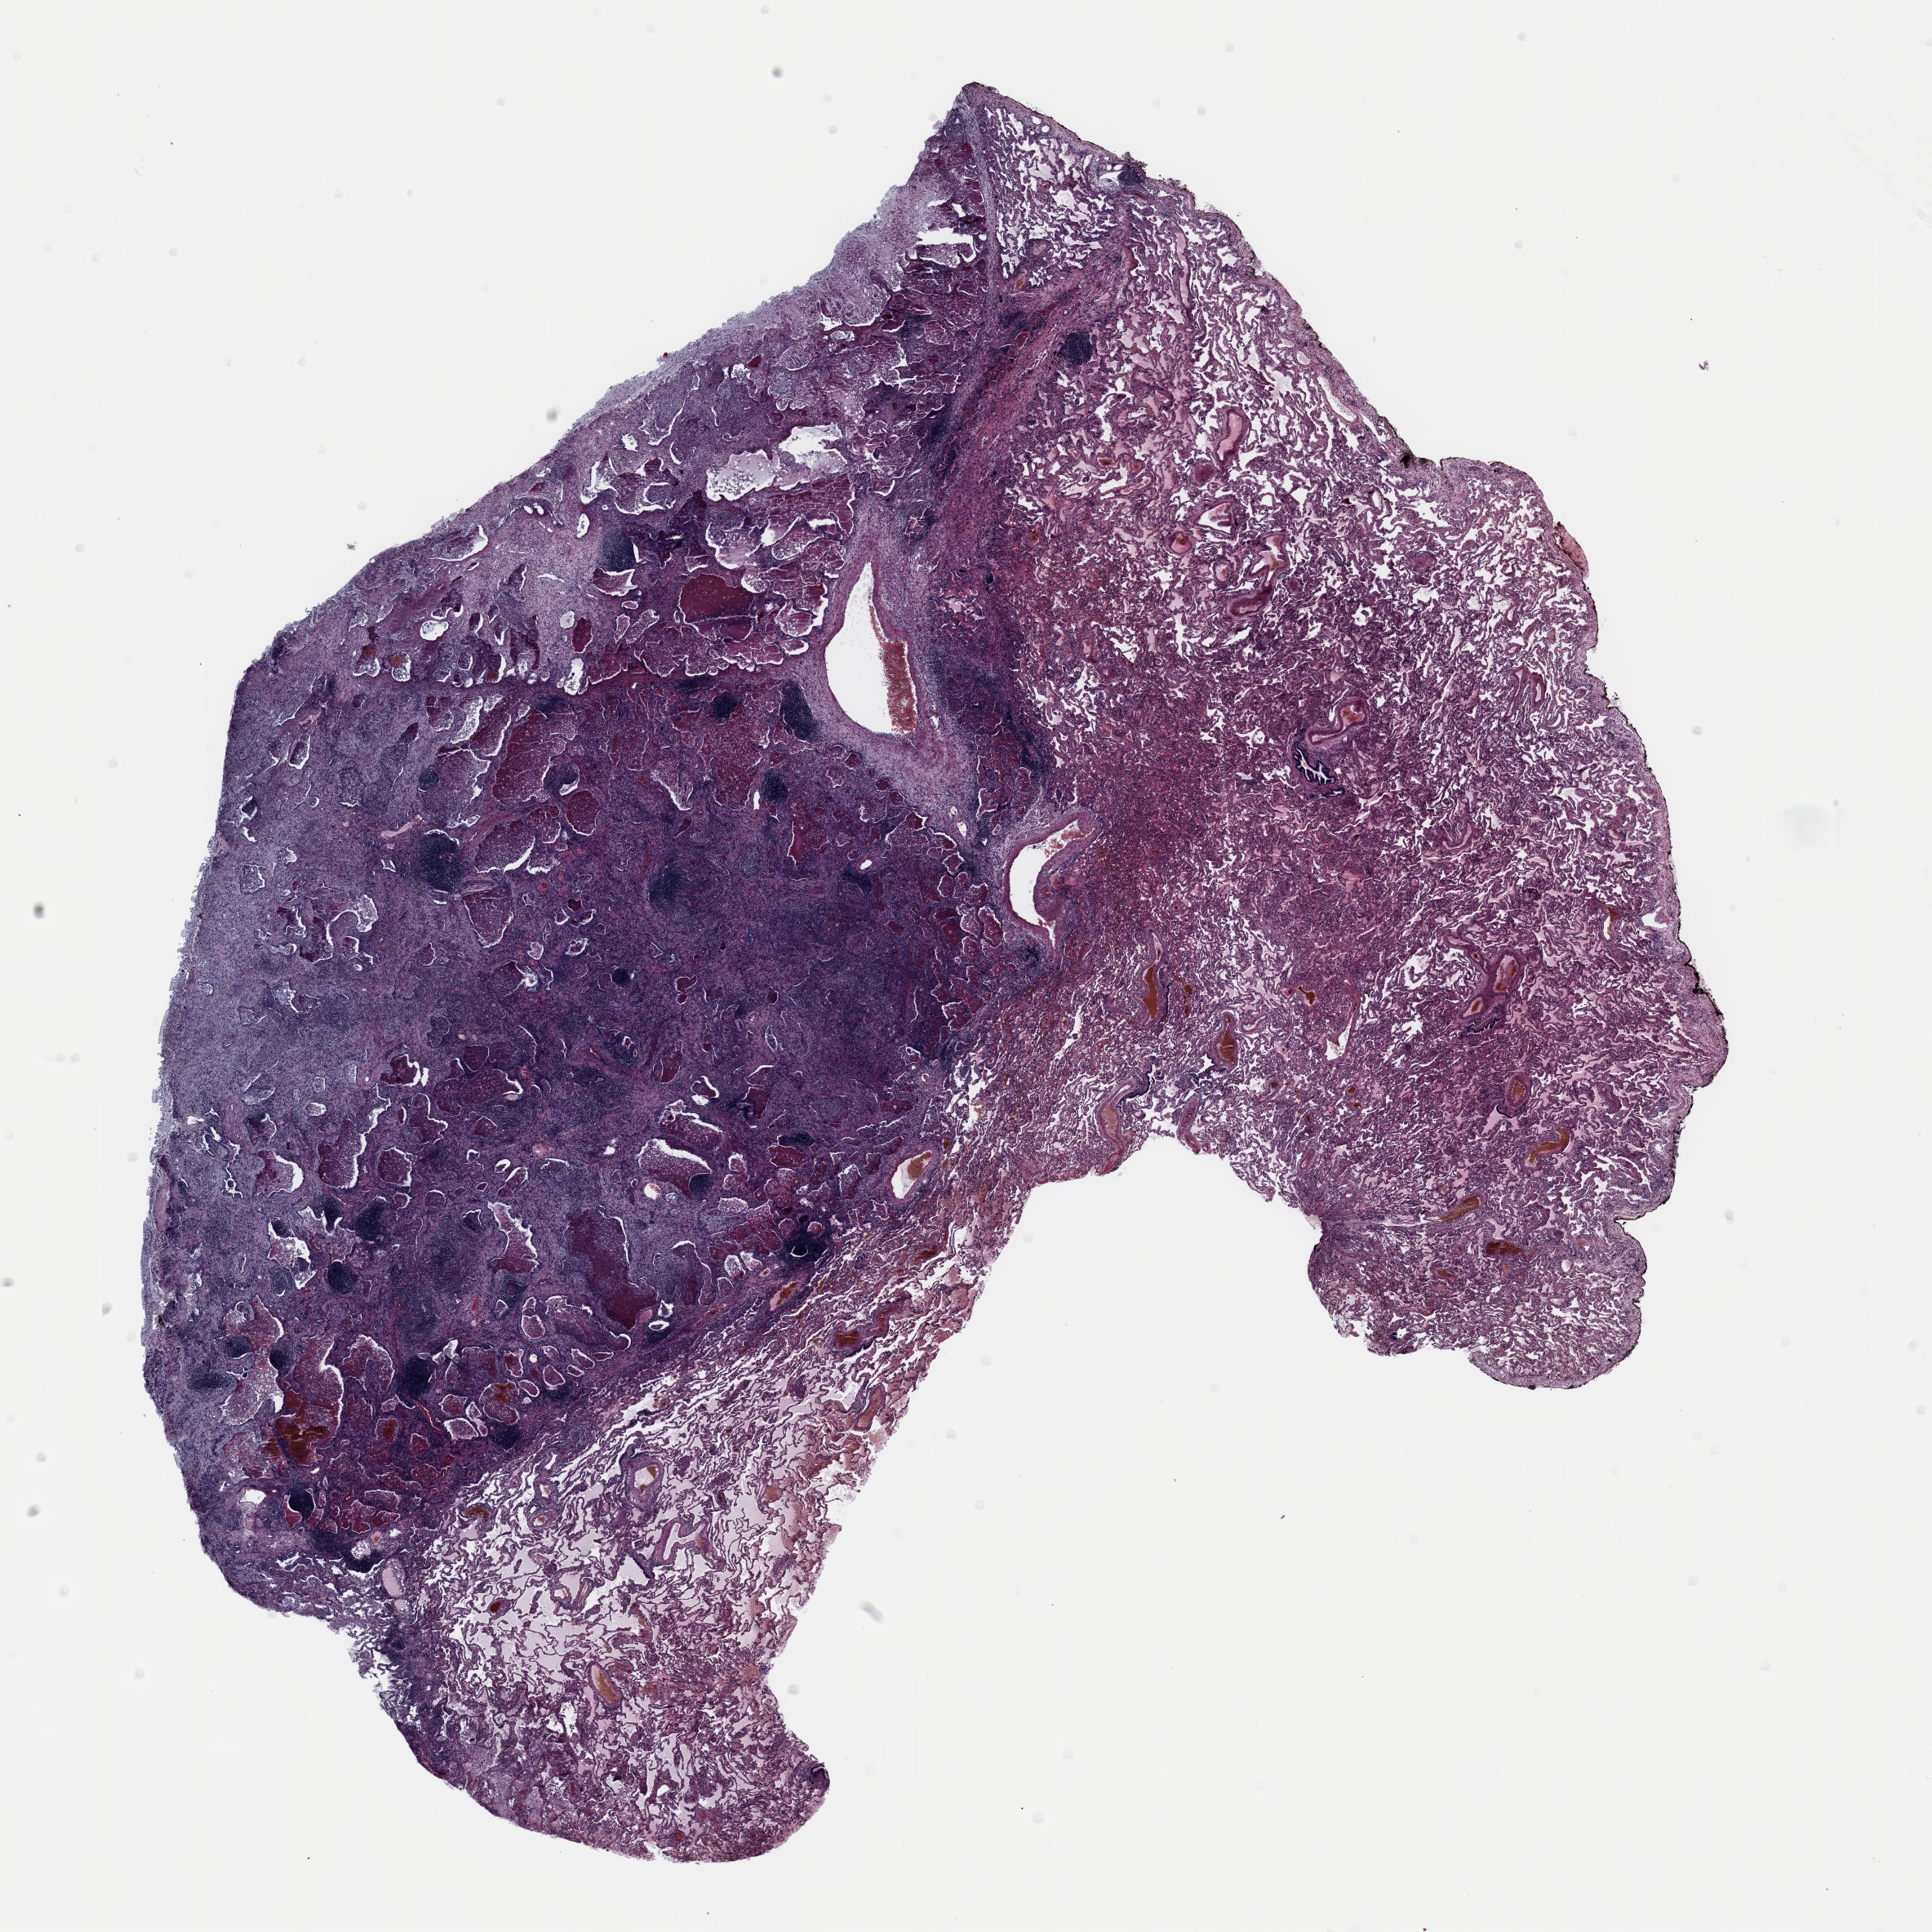
Whole-slide histology image, H&E-stained, low-resolution overview of the scanned area, about 19.0 x 19.0 mm; formalin-fixed paraffin-embedded (FFPE) section; lung. Female, age 58 at enrolment. Former smoker at enrolment. Grade: poorly differentiated (G3).
Participant's lung-cancer diagnosis: Large cell carcinoma, NOS. Stage (AJCC 6th edition): IIIA. ICD-O-3 topography: lower lobe of lung (C34.3). Tumour size (pathology): 50 mm. Primary tumour location (clinical record): left lower lobe.